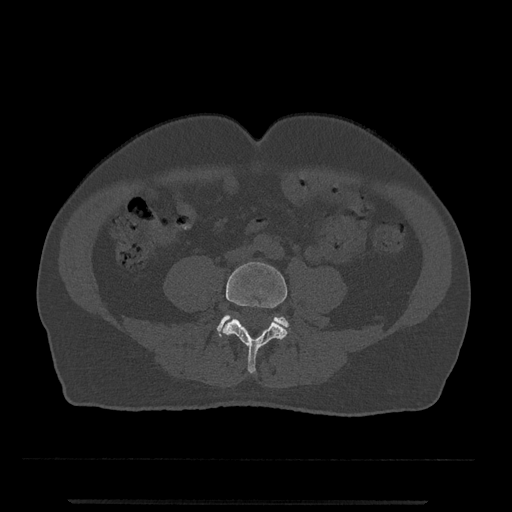
CT including the spine, one axial slice. Slice 119 of 797 in the series (ordered by position). Reconstruction kernel Br40s/3. 120 kVp. Bone window (W 1800 / L 400 HU). 512 × 512 image matrix, field of view 419 × 419 mm. Patient: male, 63 years. From the clinical record (not read from this slice): primary cancer: prostate.
Outlined on this slice (semi-automatic segmentation, software-assisted and operator-edited):
- L4 vertebra: bounding box [x1, y1, x2, y2] px = [222, 262, 288, 374]
- L5 vertebra: [217, 315, 289, 337]